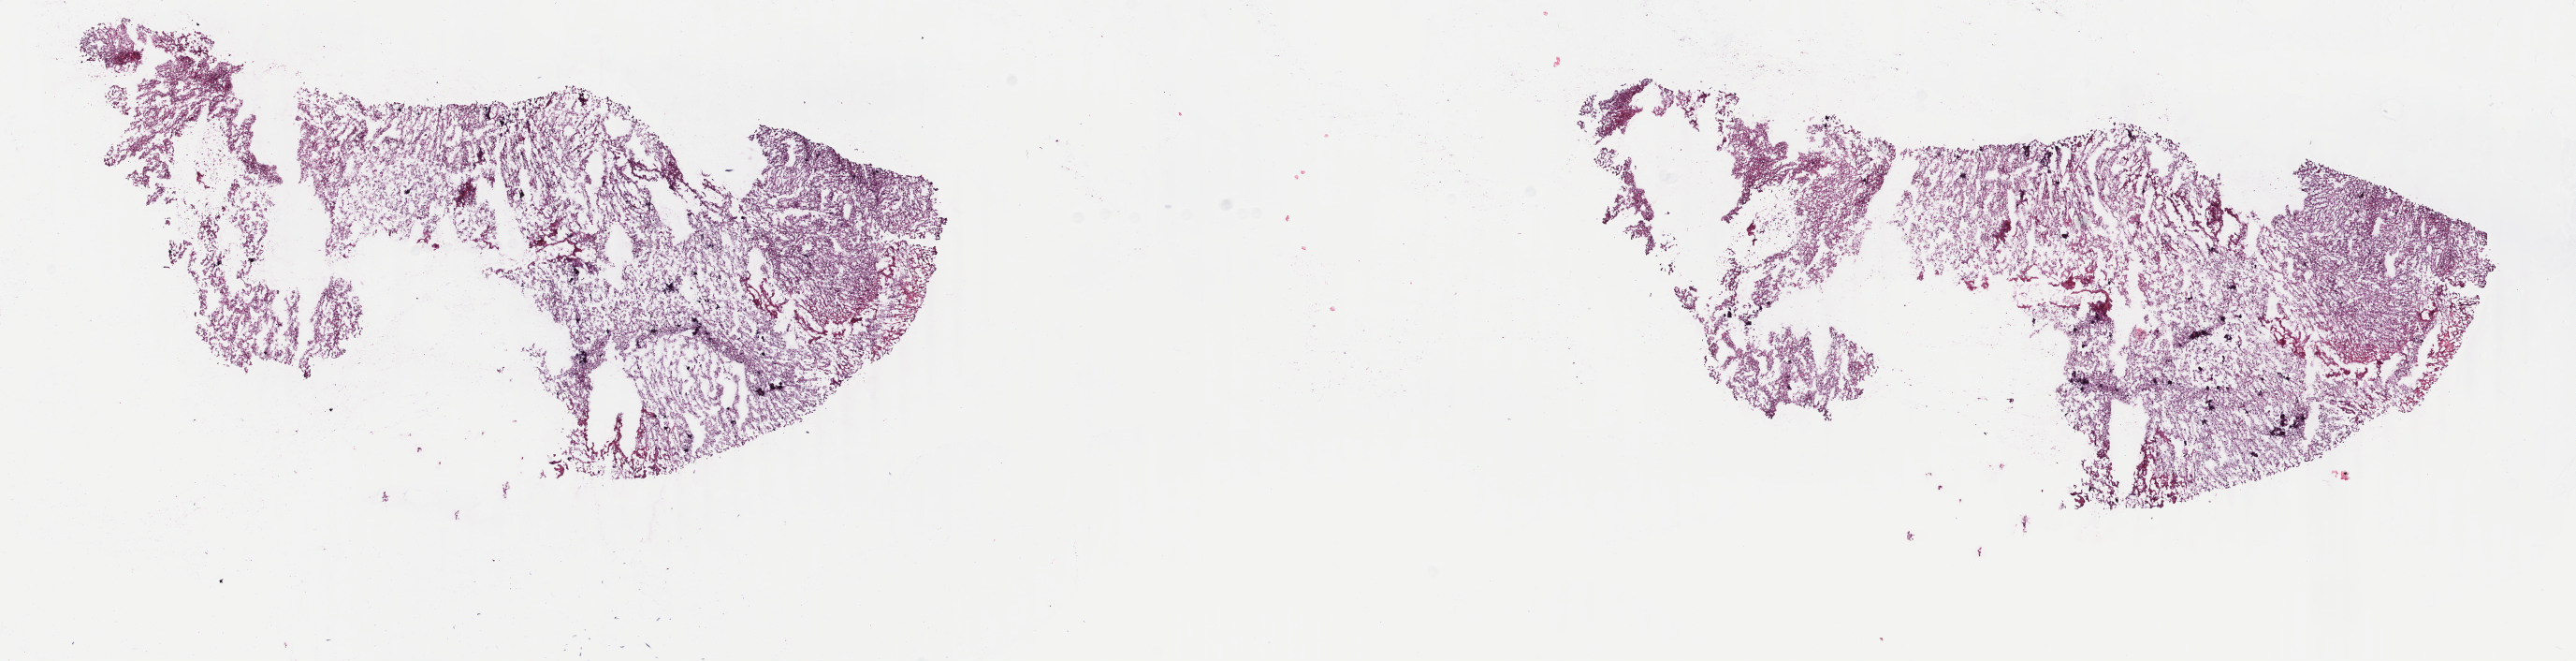
H&E whole-slide image, shown as a low-resolution overview of the whole scanned area (about 21.9 x 5.6 mm); frozen section; sample: primary tumour, brain. Patient: female, age at initial diagnosis 38 years. Histologic grade: G3 (poorly differentiated). Pathologist review of this section (percent, as recorded): tumour cells 65%, tumour nuclei 75%, normal cells 10%, stromal cells 15%, necrosis 10%. Infiltration values recorded for this section: lymphocyte infiltration 0%, monocyte infiltration 0%, neutrophil infiltration 0%.
• laterality: left
• histologic diagnosis: Oligodendroglioma, anaplastic